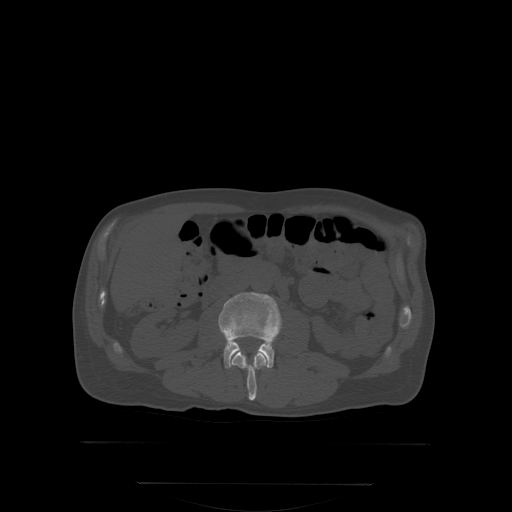
CT including the spine, one axial slice; slice 129 of 350 in the series (ordered by position); bone window (W 1800 / L 400 HU); 512 × 512 image matrix, field of view 500 × 500 mm. Patient: male, 58 years. Case-level facts recorded for this patient, not image findings: primary cancer: prostate; vertebrae with lytic lesions (as recorded): L1.
Structures marked on this image (semi-automatic segmentation, software-assisted and operator-edited):
- L2 vertebra: bounding box <231,350,268,401> (left, top, right, bottom; pixels)
- L3 vertebra: <220,293,282,368>